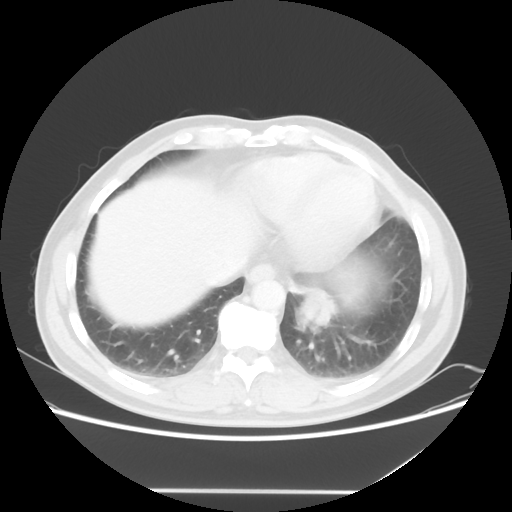
Chest CT, one axial slice; slice 15 of 56 in the series (ordered by position); 120 kVp; lung window (W 1500 / L -600 HU); 5 mm slice thickness; 512 × 512 image matrix, field of view 385 × 385 mm. Patient: male, 61 years. Case-level facts recorded for this patient, not image findings: clinical TNM (as recorded): T1c N0 M0.
Outlined on this slice (rectangle marked by the reading radiologist):
- lung tumour (recorded histology: adenocarcinoma): box from (x=286, y=282) to (x=339, y=339) px